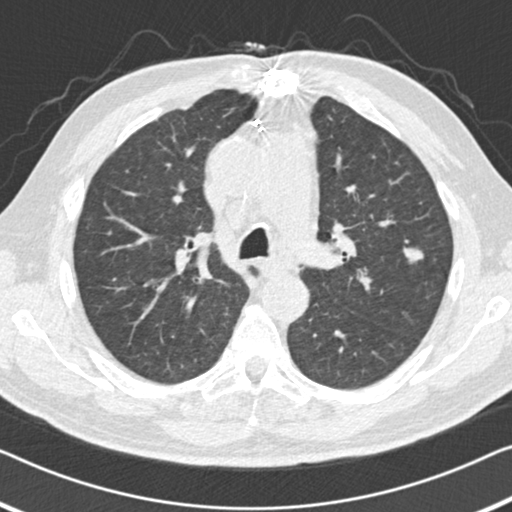
Low-dose screening chest CT, one axial slice. Slice 104 of 155 in the series (ordered by position). Reconstruction kernel B30f. Lung window (W 1500 / L -600 HU). 512 × 512 image matrix.
Structures marked on this image (expert manual segmentation):
- lesion 1 (tumor, upper lobe of left lung): box from (x=403, y=247) to (x=424, y=264) px